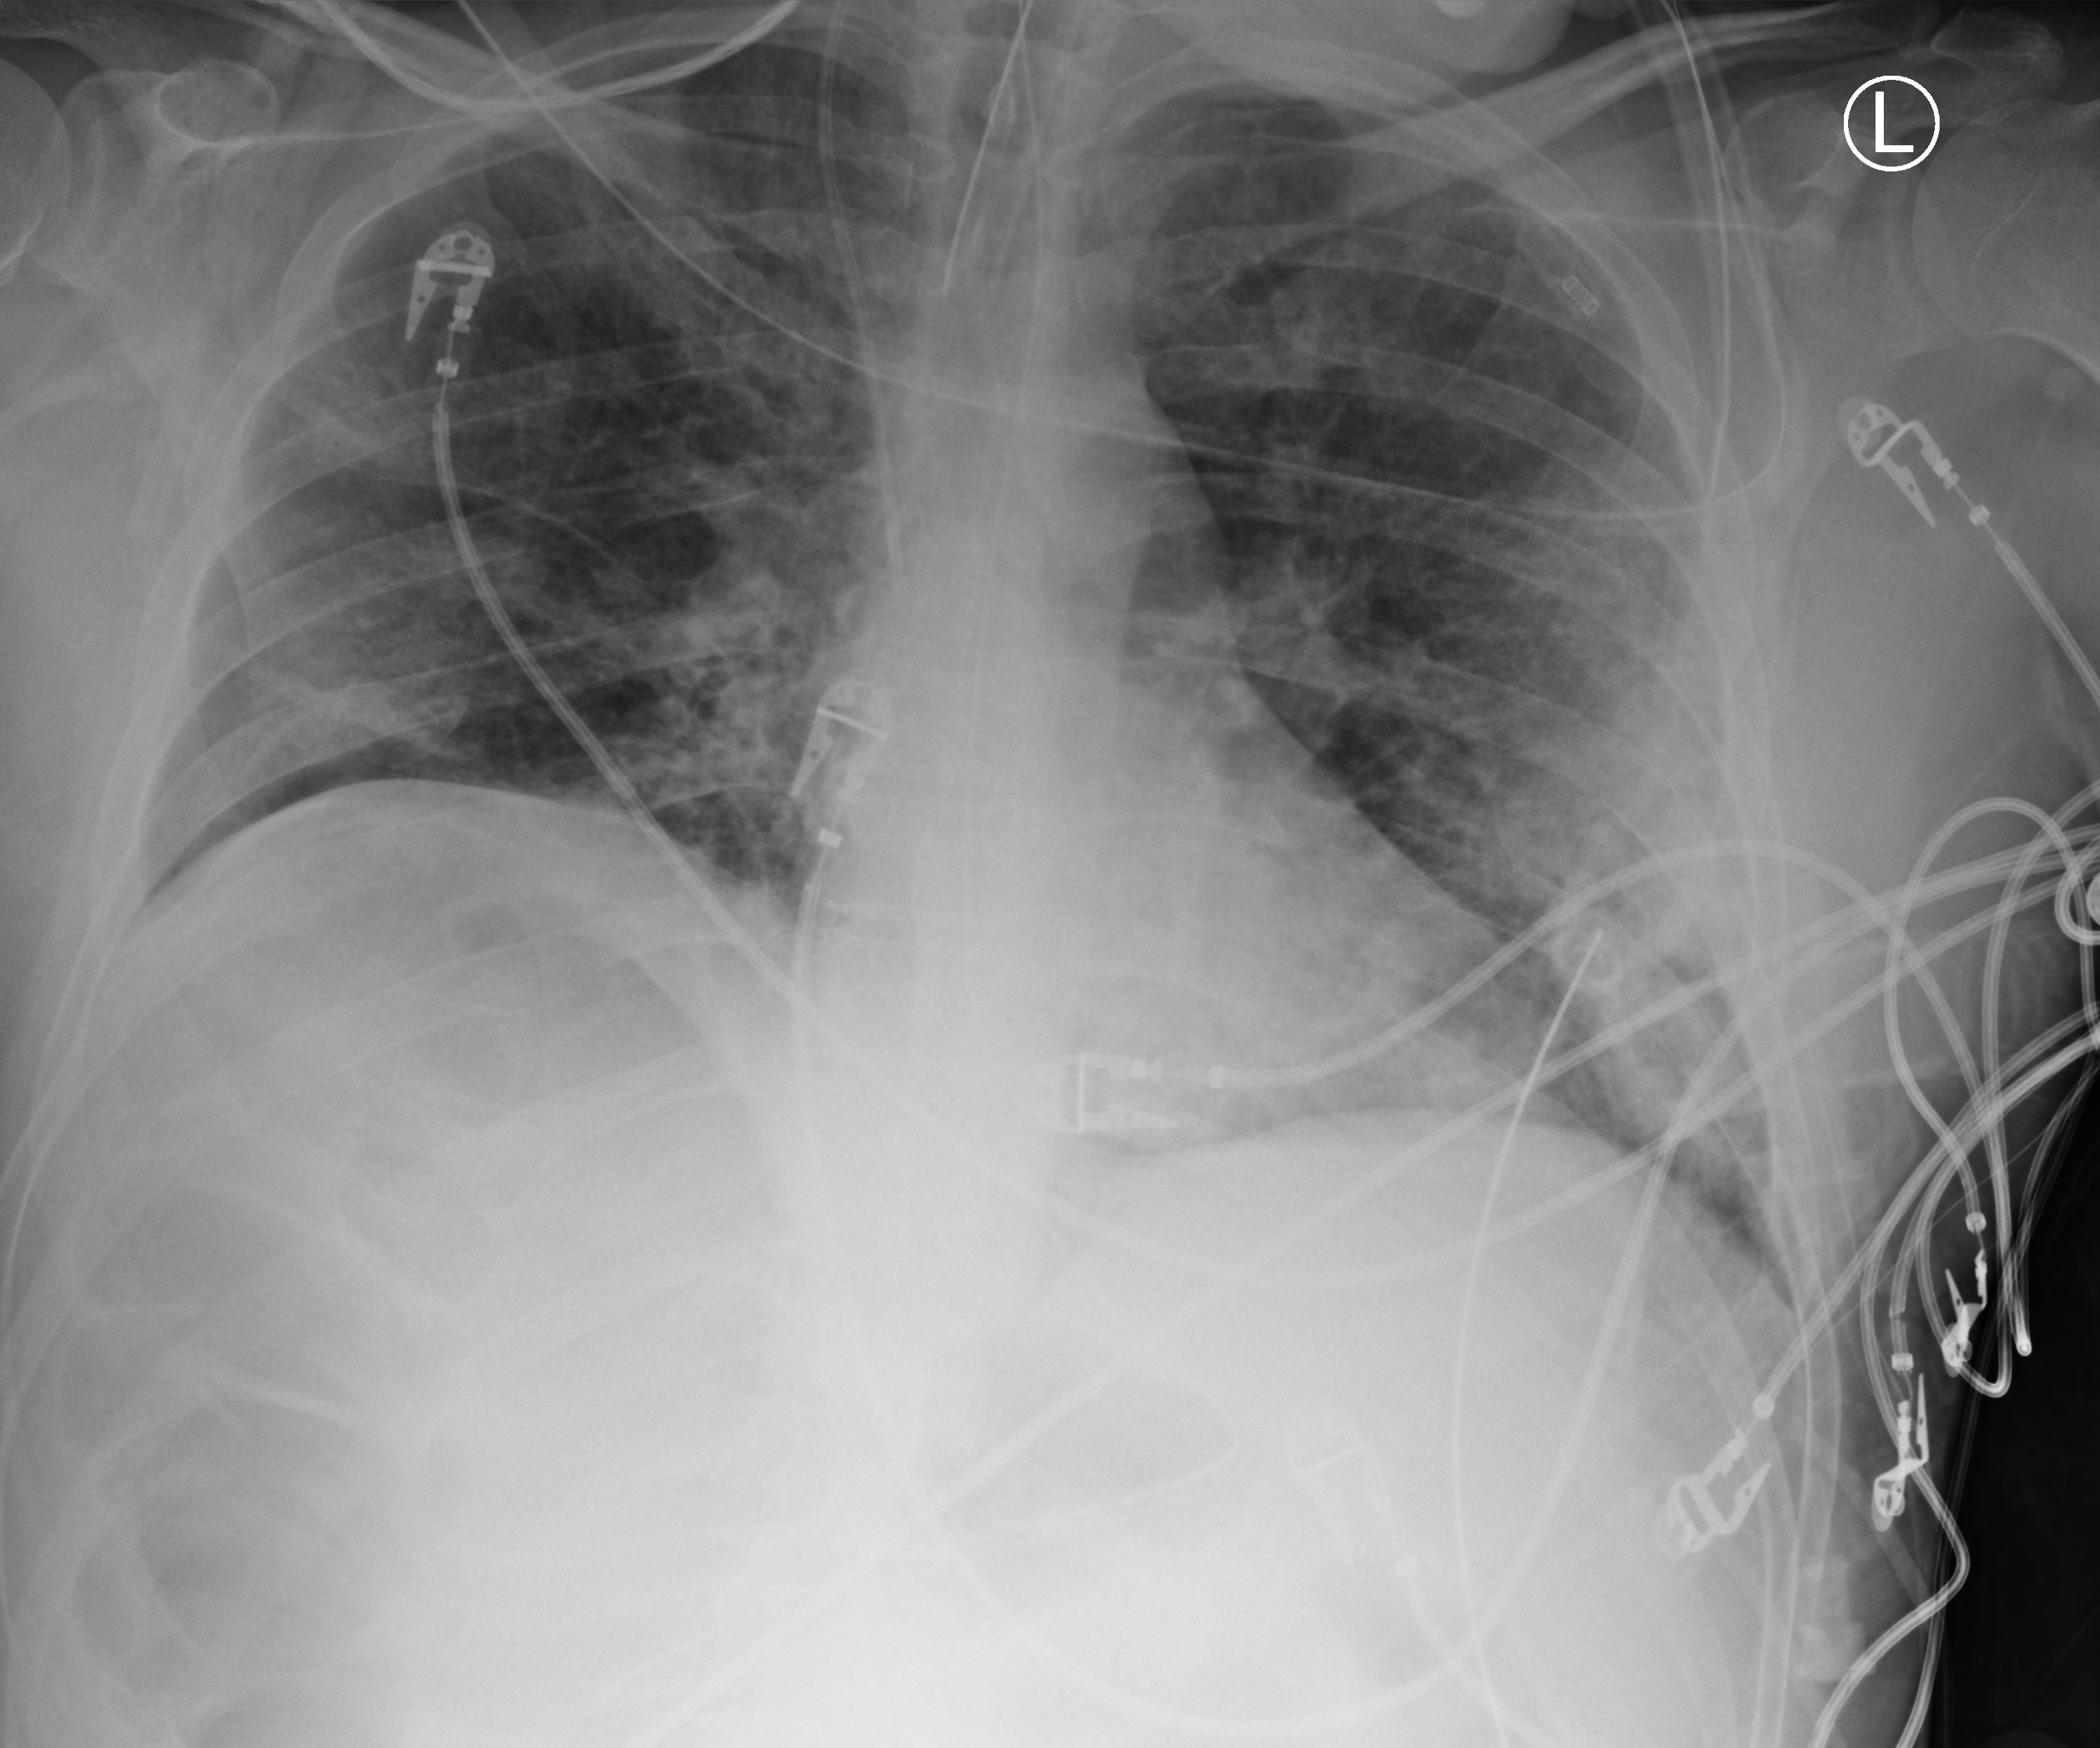
Bedside chest radiograph (computed radiography); anteroposterior (AP) projection. Patient hospitalised with COVID-19; male, aged 18–59 years.
From the hospital-stay record, not from the radiograph (when in the stay this image was taken is not recorded):
- chronic kidney disease (admission record): no
- admitted to intensive care during this hospital stay: yes
- length of hospital stay: 48 days